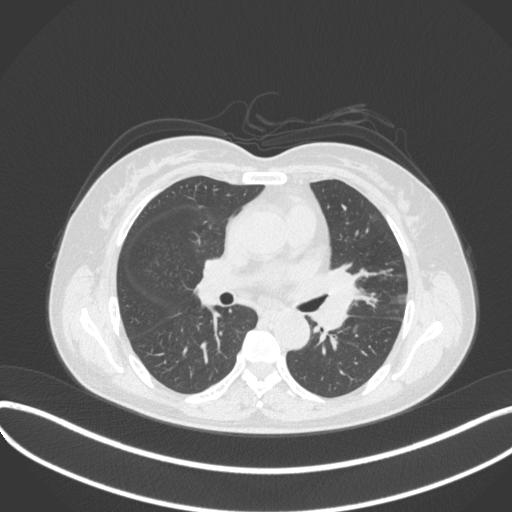
Chest CT, one axial slice. Slice 194 of 373 in the series (ordered by position). Reconstruction kernel B31f. Lung window (W 1500 / L -600 HU). 512 × 512 image matrix. Patient: female, 54 years. From the clinical record (not read from this slice): clinical TNM (as recorded): T2a N1 M0.
Structures marked on this image (rectangle marked by the reading radiologist):
- lung tumour (recorded histology: small cell carcinoma): bounding box [x1, y1, x2, y2] px = [316, 258, 362, 340]